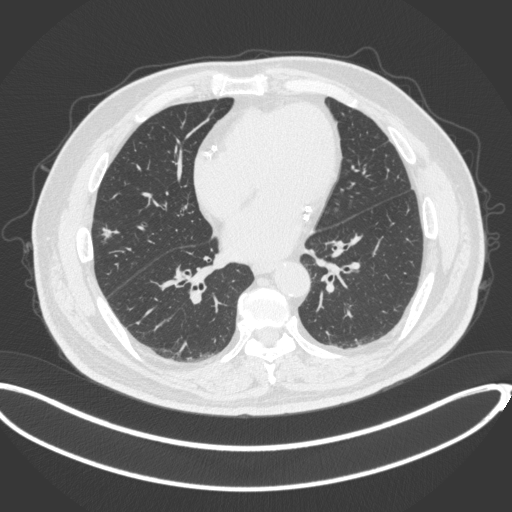
Chest CT, one axial slice; reconstruction kernel B31f; 120 kVp; lung window (W 1500 / L -600 HU); 512 × 512 image matrix, field of view 427 × 427 mm. Patient: male, 68 years. From the clinical record (not read from this slice): clinical TNM (as recorded): T1c N0 M0; histopathological grade: G2.
Annotated regions visible in this slice (rectangle marked by the reading radiologist):
- lung tumour (recorded histology: adenocarcinoma): bounding box <102,225,113,242> (left, top, right, bottom; pixels)